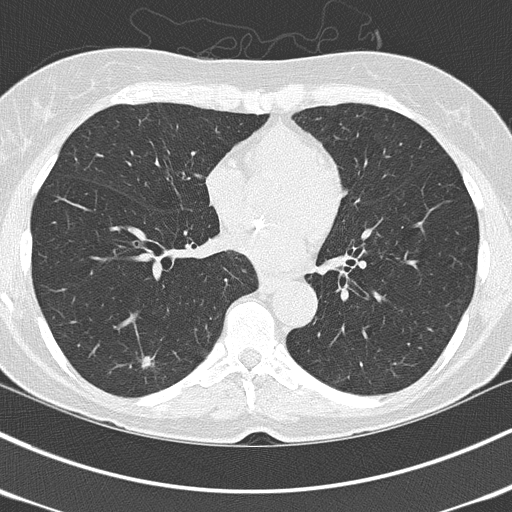
Chest CT (low-dose screening protocol), one axial image; third annual screen; lung window (W 1500 / L -600 HU); lung (sharp) reconstruction kernel (B50f); slice 90 of 150 in the series; 512 × 512 image matrix, field of view 318 × 318 mm. Female participant, aged 67 years at enrolment. Current smoker at enrolment.
Expert reader's lesion annotation, box from (x=130, y=347) to (x=168, y=380) px. The screening reader recorded 3 non-calcified nodules or masses ≥4 mm on this exam (right lower lobe, right lower lobe, left lower lobe); which of them this box marks is not recorded. Later outcome: lung cancer diagnosed 64 days after this screen — adenocarcinoma, NOS, left lower lobe, poorly differentiated (G3), stage IA (AJCC 6th edition), 25 mm at pathology.